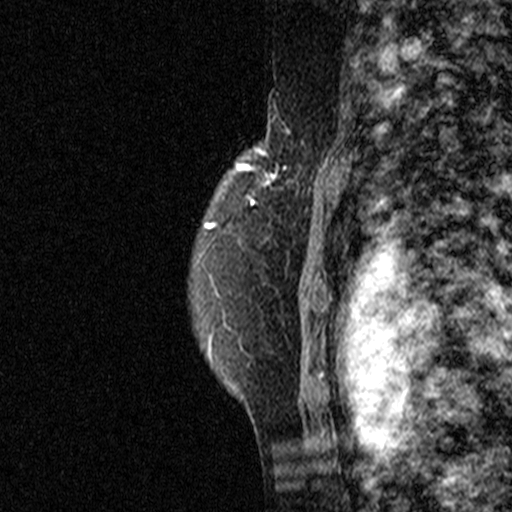
Breast MRI (dynamic contrast-enhanced), one sagittal slice; position 34 of 44 along the scan axis; dynamic contrast-enhanced study with each time point stored as its own series, time point 2 of 3 at this slice position (early post-contrast, ordered by acquisition time); 1.5 T; TE 4.5 ms, TR 11 ms; 3 mm slice thickness; 512 × 512 image matrix, field of view 200 × 200 mm. Patient: female, 49 years. From the clinical record (not read from this slice): setting: breast cancer imaged before/during neoadjuvant chemotherapy; receptor status: triple-negative.
Outlined on this slice (semi-automatically segmented with operator editing):
- analysis volume of interest (the breast-tissue region the enhancement analysis was run in; not a lesion): bounding box (x1, y1, x2, y2) in pixels: (264, 122, 331, 227)
- tumour enhancement mask (voxels above the 90 % enhancement threshold inside the analysis volume of interest): (270, 167, 299, 184)